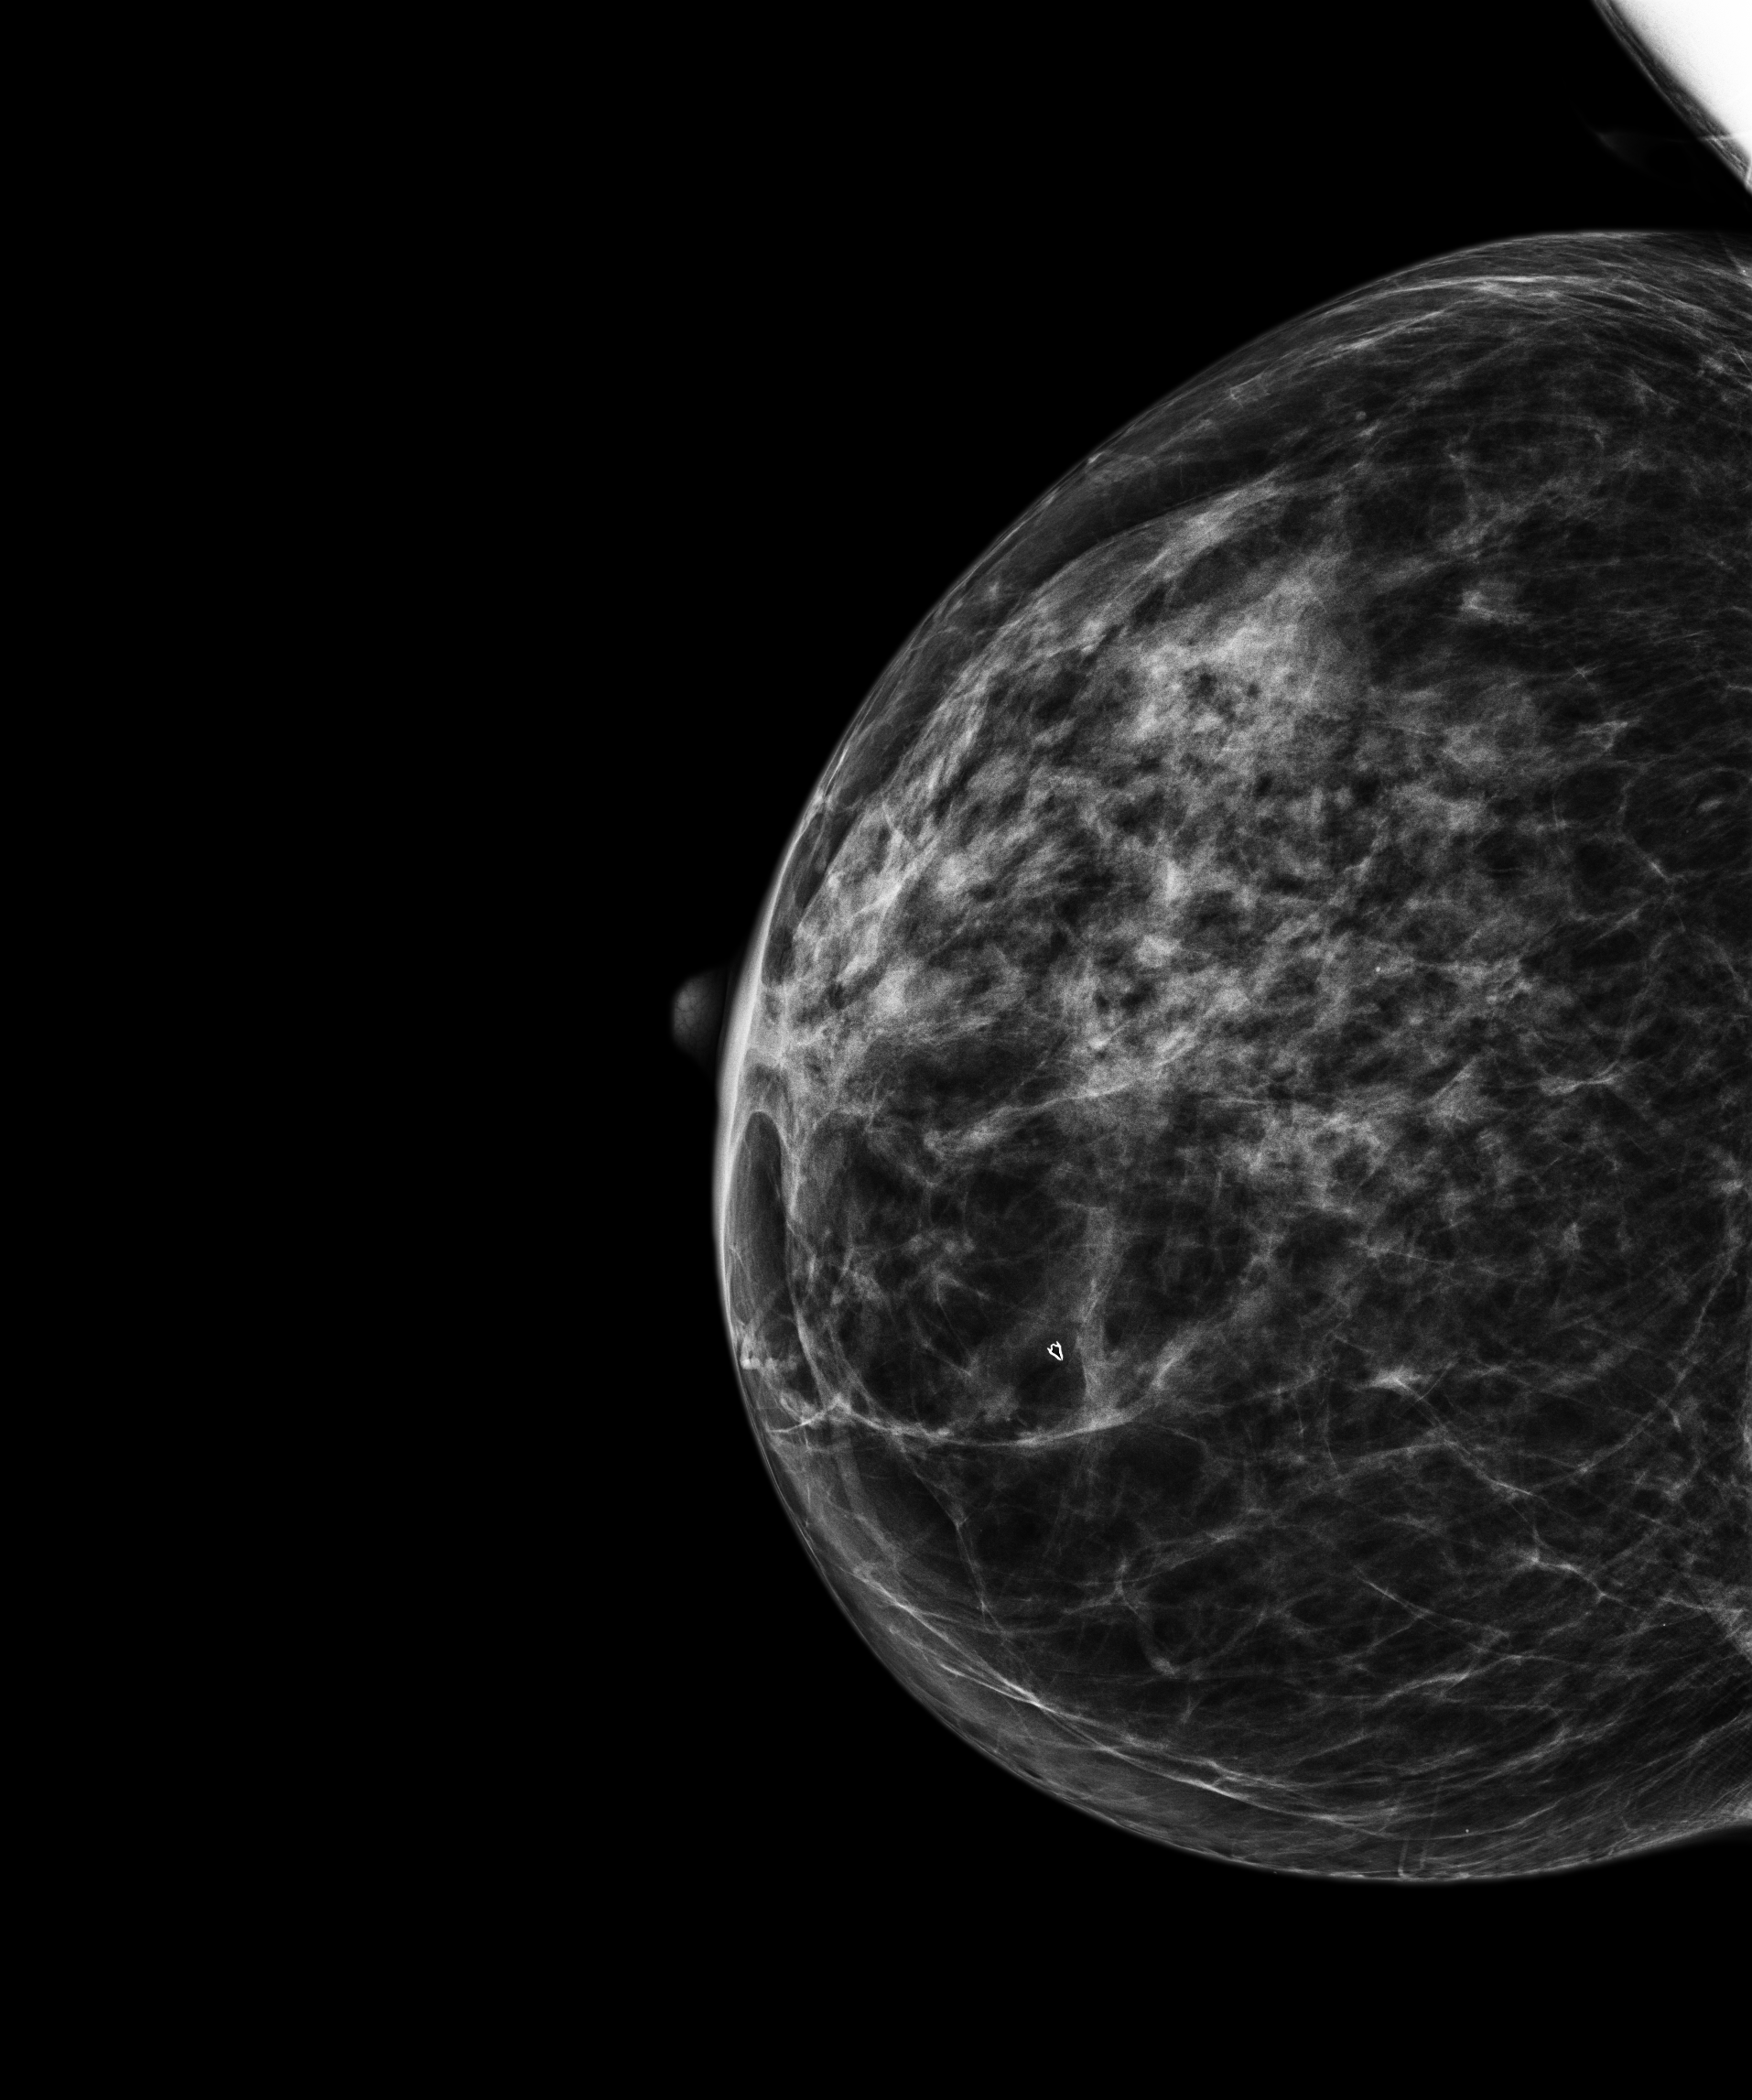
Full-field digital mammogram (FFDM); right breast; craniocaudal (CC) view; annual screening mammography examination; compressed breast thickness 41 mm. Patient aged 56 years (female).
- BI-RADS breast density category at the screening exam (both breasts, scale 1–4): 3
- final BI-RADS assessment for this screening round (tomosynthesis exam, both breasts): category 1
- recall: no recall after this screen